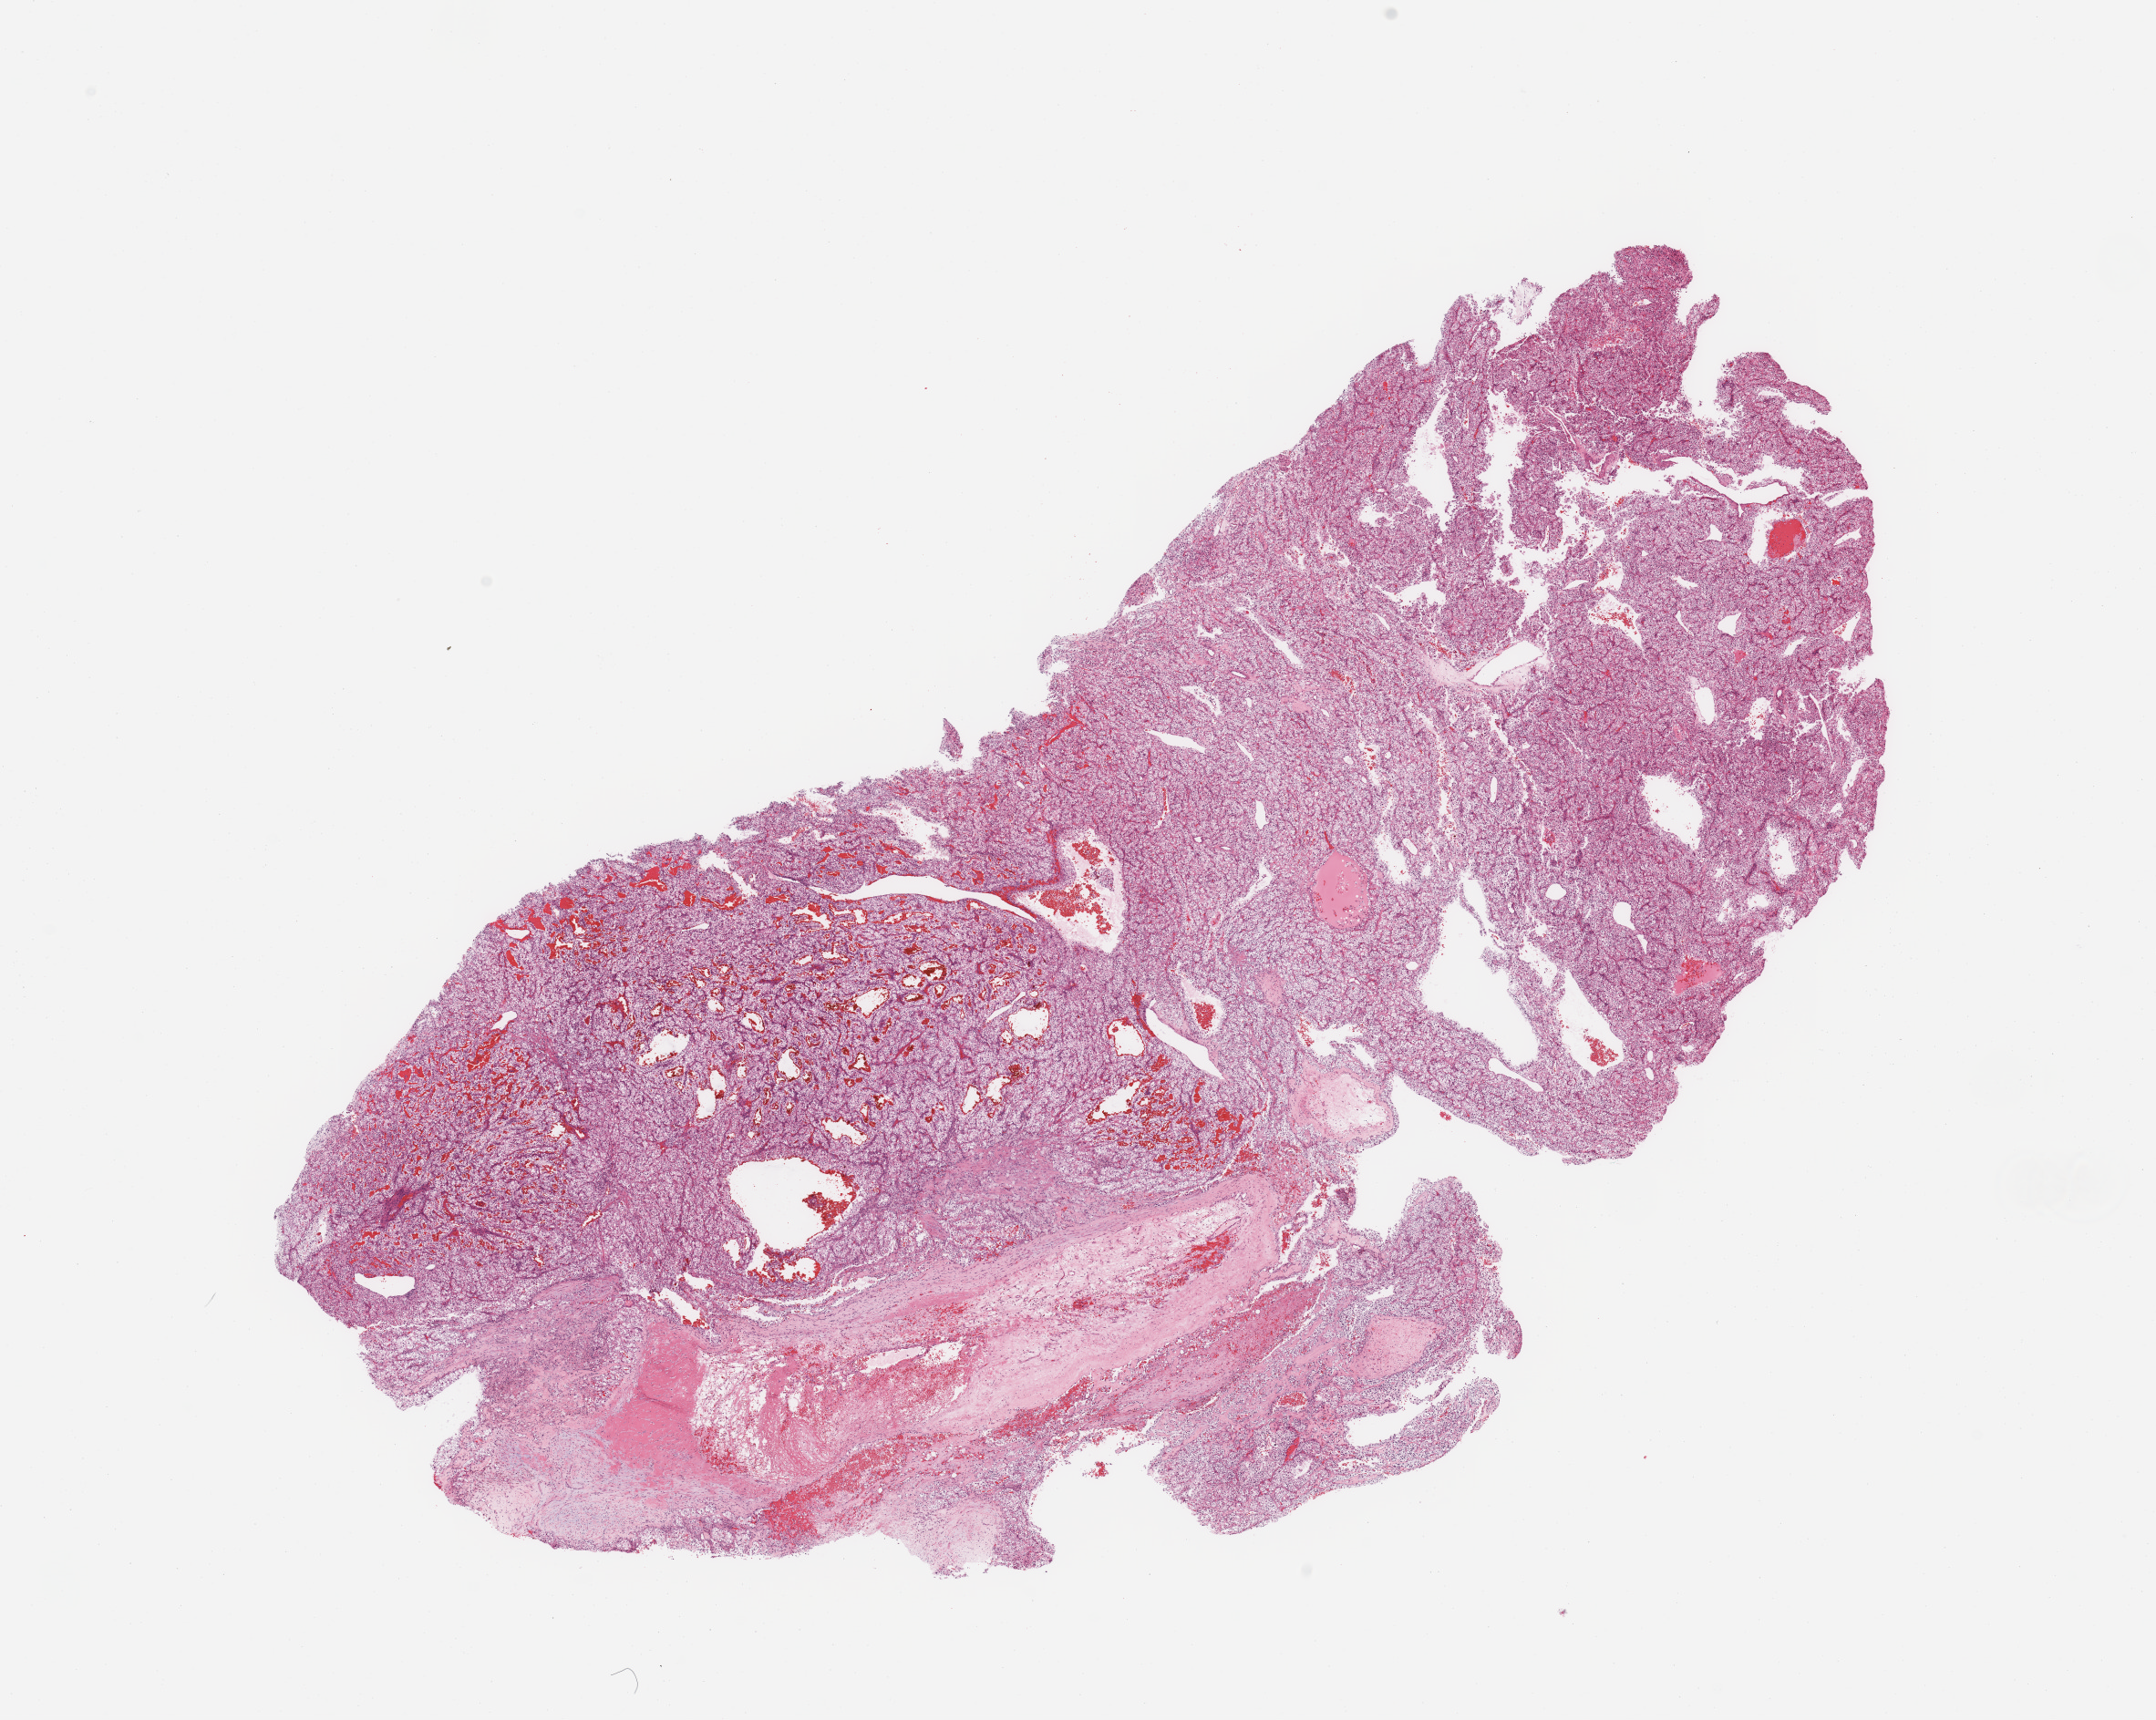
Hematoxylin and eosin (H&E) stained whole-slide image, shown as a low-resolution overview of the whole scanned area (about 18.7 x 14.9 mm), tumour tissue sample, sampled site: kidney. Patient: male, age 63 years. Histologic grade: G4 (undifferentiated). Slide review estimates, as recorded: tumour nuclei 85%, necrosis 5%.
* histologic diagnosis: Renal cell carcinoma, NOS
* AJCC pathologic stage: III